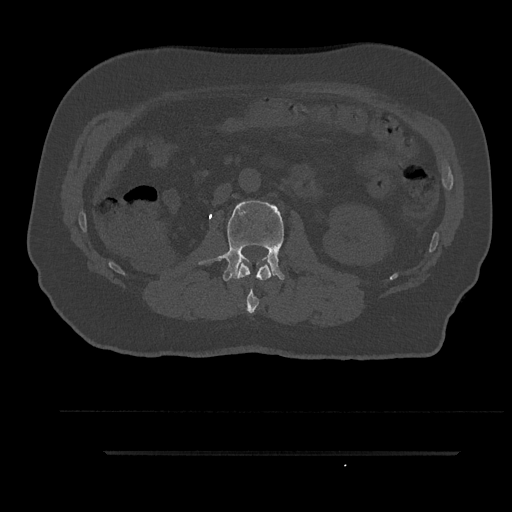
CT including the spine, one axial slice; slice 129 of 797 in the series (ordered by position); reconstruction kernel Br40s/3; bone window (W 1800 / L 400 HU); 0.5 mm slice thickness; 512 × 512 image matrix. Patient: male, 63 years. Case-level facts recorded for this patient, not image findings: primary cancer: renal; vertebrae with lytic lesions (as recorded): T8.
Outlined on this slice (semi-automatically segmented with operator editing):
- L1 vertebra: bounding box <235,262,273,314> (left, top, right, bottom; pixels)
- L2 vertebra: <199,201,285,281>